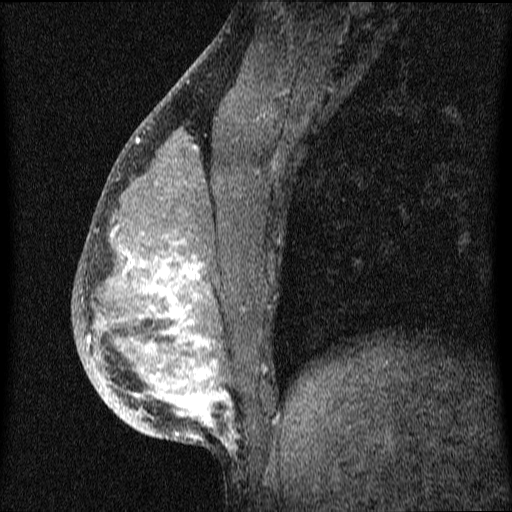
Breast MRI (dynamic contrast-enhanced), one sagittal slice; position 27 of 64 along the scan axis; dynamic contrast-enhanced series, image 2 of 4 at this slice position (ordered by acquisition); 1.5 T; TE 4.2 ms, TR 9.1 ms; 2 mm slice thickness; 512 × 512 image matrix, field of view 180 × 180 mm. Female patient, age 33 years.
Outlined on this slice (semi-automatic segmentation, software-assisted and operator-edited):
- analysis volume of interest (the breast-tissue region the enhancement analysis was run in; not a lesion): bounding box (x1, y1, x2, y2) in pixels: (73, 151, 336, 458)
- tumour enhancement mask (voxels above the 70 % enhancement threshold inside the analysis volume of interest): (88, 227, 233, 447)